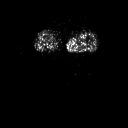
FDG PET of an extremity soft-tissue mass (from a PET/CT study), one axial slice. Slice 1 of 91 in the series (ordered by position). 3.27 mm slice thickness. 128 × 128 image matrix, field of view 700 × 700 mm. Patient: female, 74 years. Case-level facts recorded for this patient, not image findings: histological type: pleomorphic leiomyosarcoma; grade: high; site of the primary tumour: left thigh.
Structures marked on this image (expert contour drawn on MRI and transferred to this co-registered scan by the dataset authors):
- gross tumour volume including surrounding oedema: bounding box (x1, y1, x2, y2) in pixels: (73, 36, 86, 49)